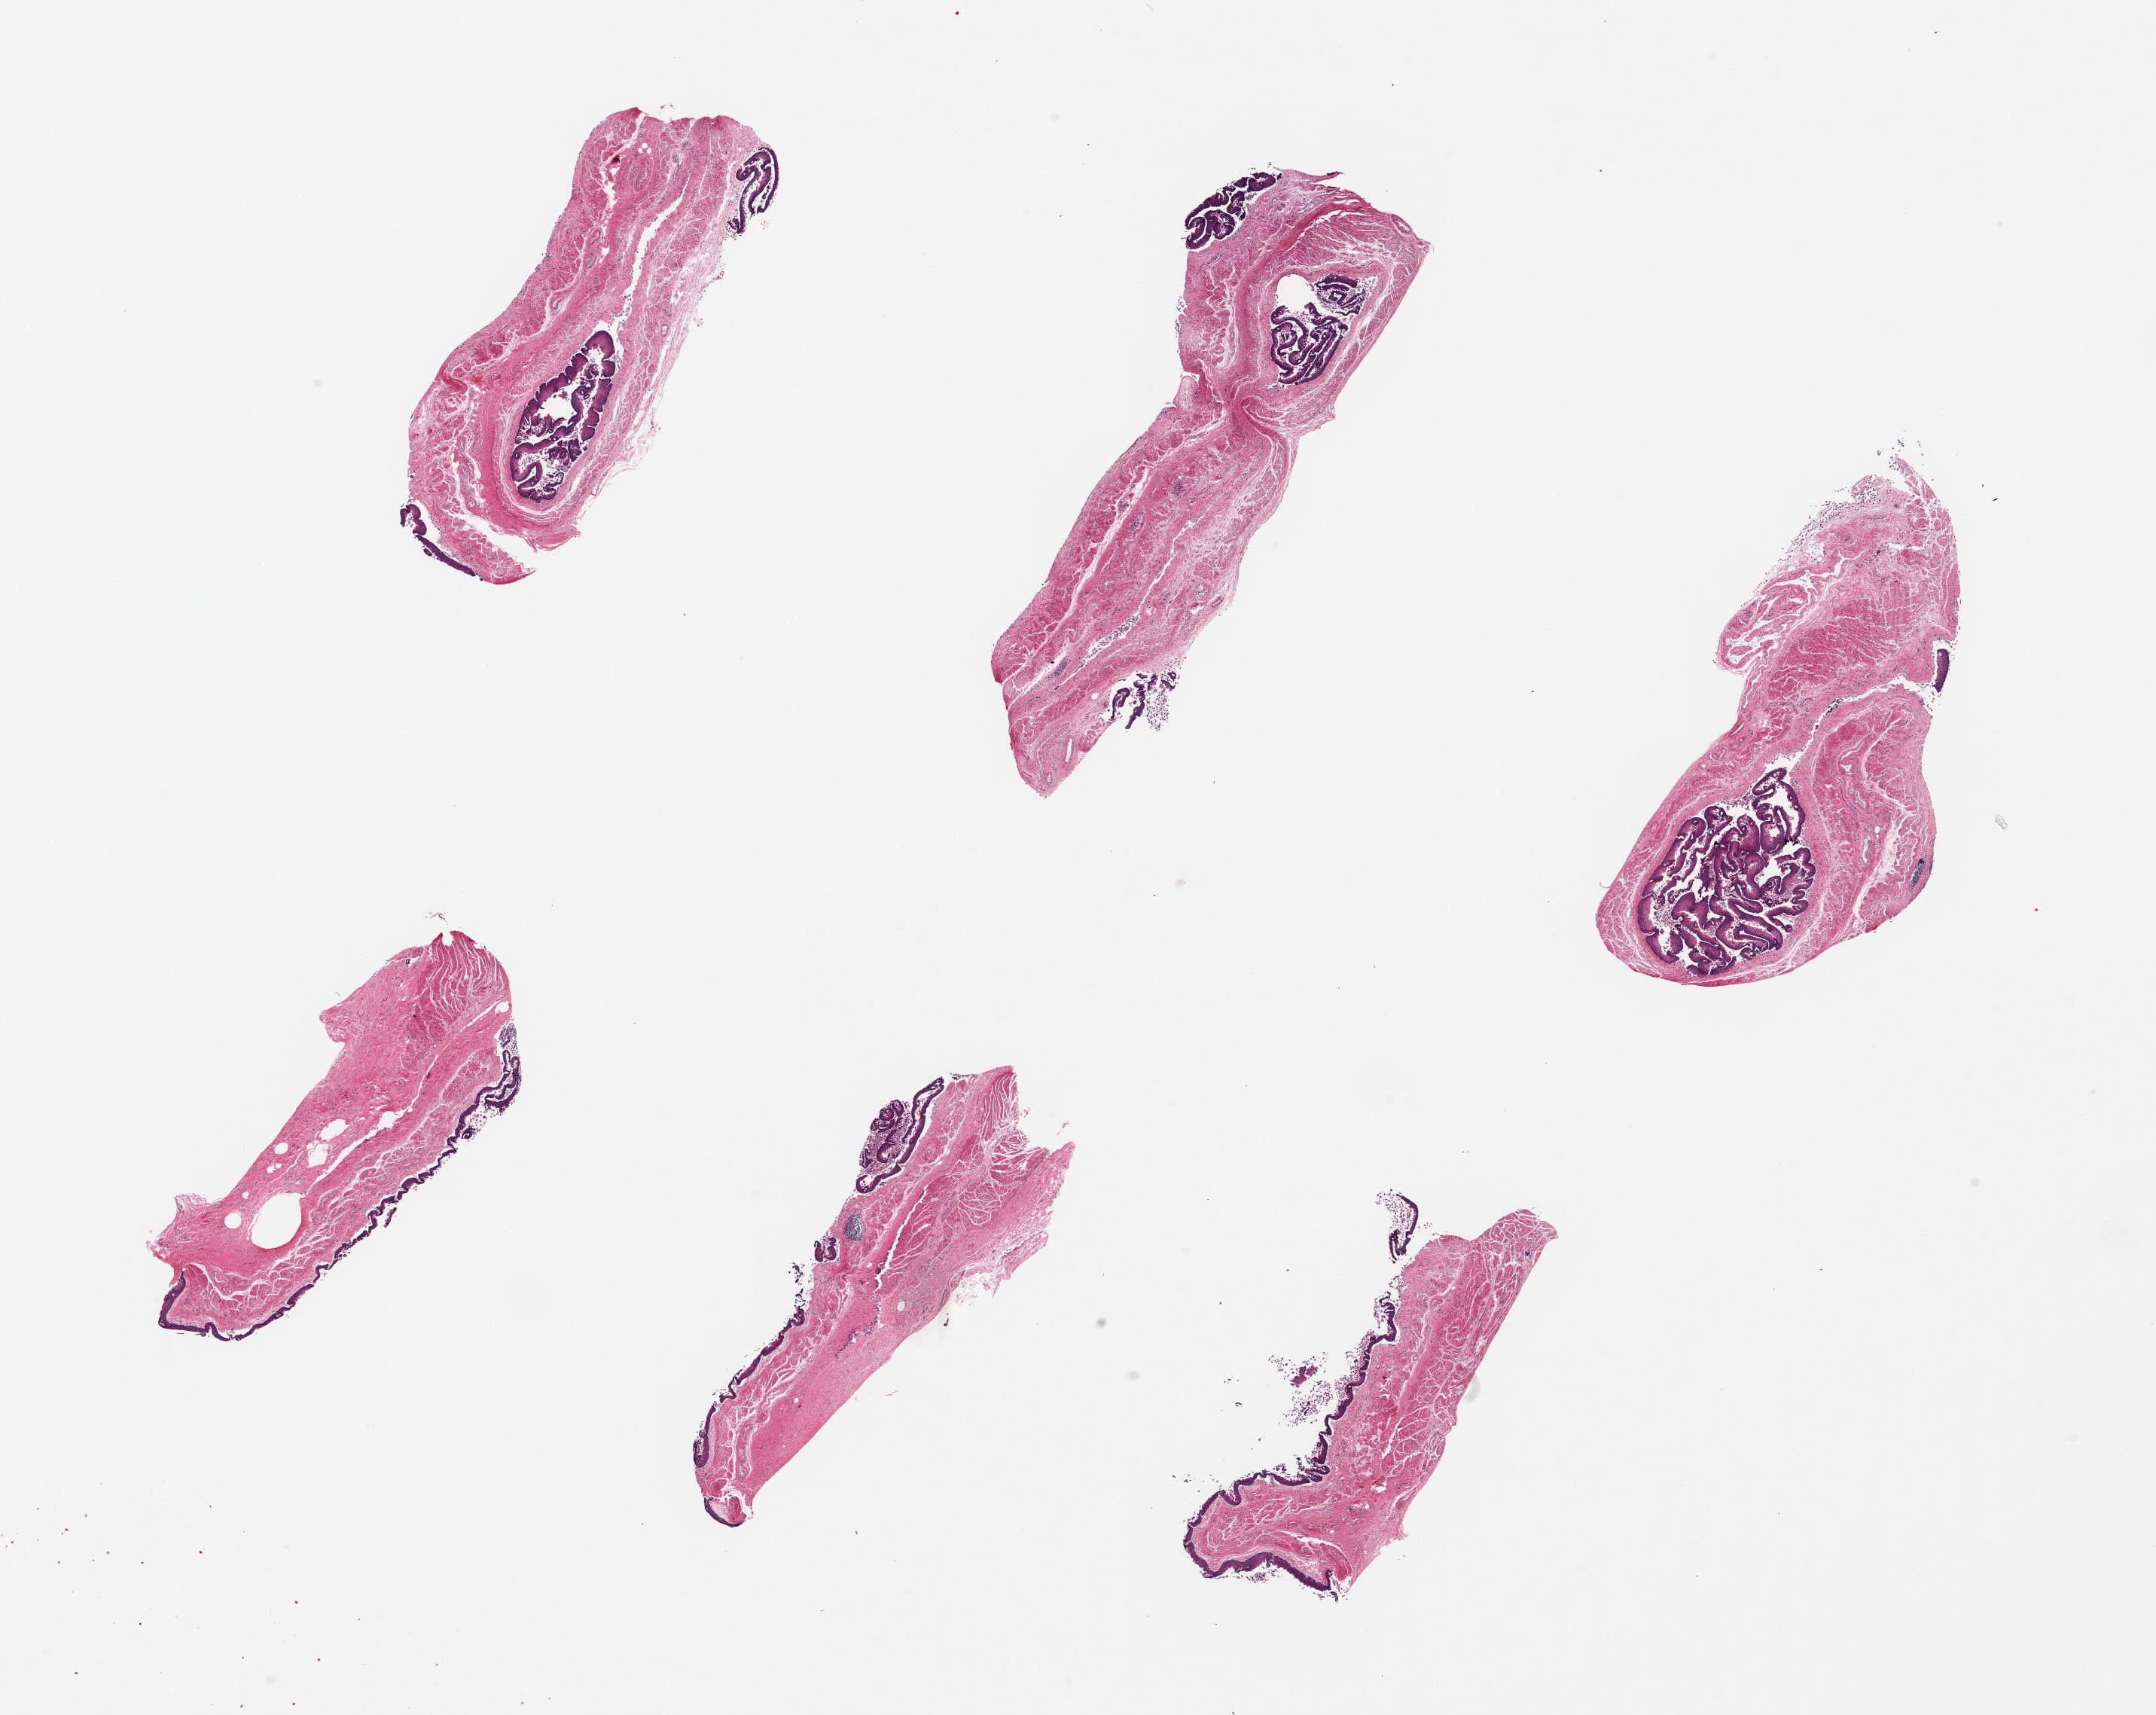
Hematoxylin and eosin (H&E) whole-slide image, brightfield, a low-resolution overview of the entire scanned area, about 22.6 x 18.0 mm. PAXgene-fixed paraffin-embedded (PFPE) section. Section of esophageal mucous membrane (target tissue). Tissue donor sample. Male donor.
• reviewer comment on this tissue sample: 6 pieces, up to 7x2.4mm; epithelial layer detached